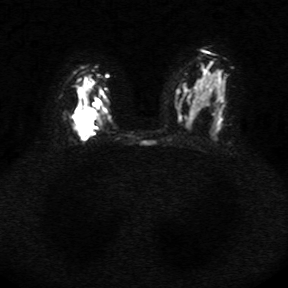
Breast MRI, one axial slice; position 17 of 34 along the scan axis; diffusion-weighted series; image 2 of 4 stored at this slice position (different b-values; order by instance number); 1.5 T; 5 mm slice thickness; 288 × 288 image matrix, field of view 340 × 340 mm. Female patient.
Outlined on this slice (manually delineated by an expert):
- tumour on diffusion-weighted imaging: bounding box <72,106,95,136> (left, top, right, bottom; pixels)